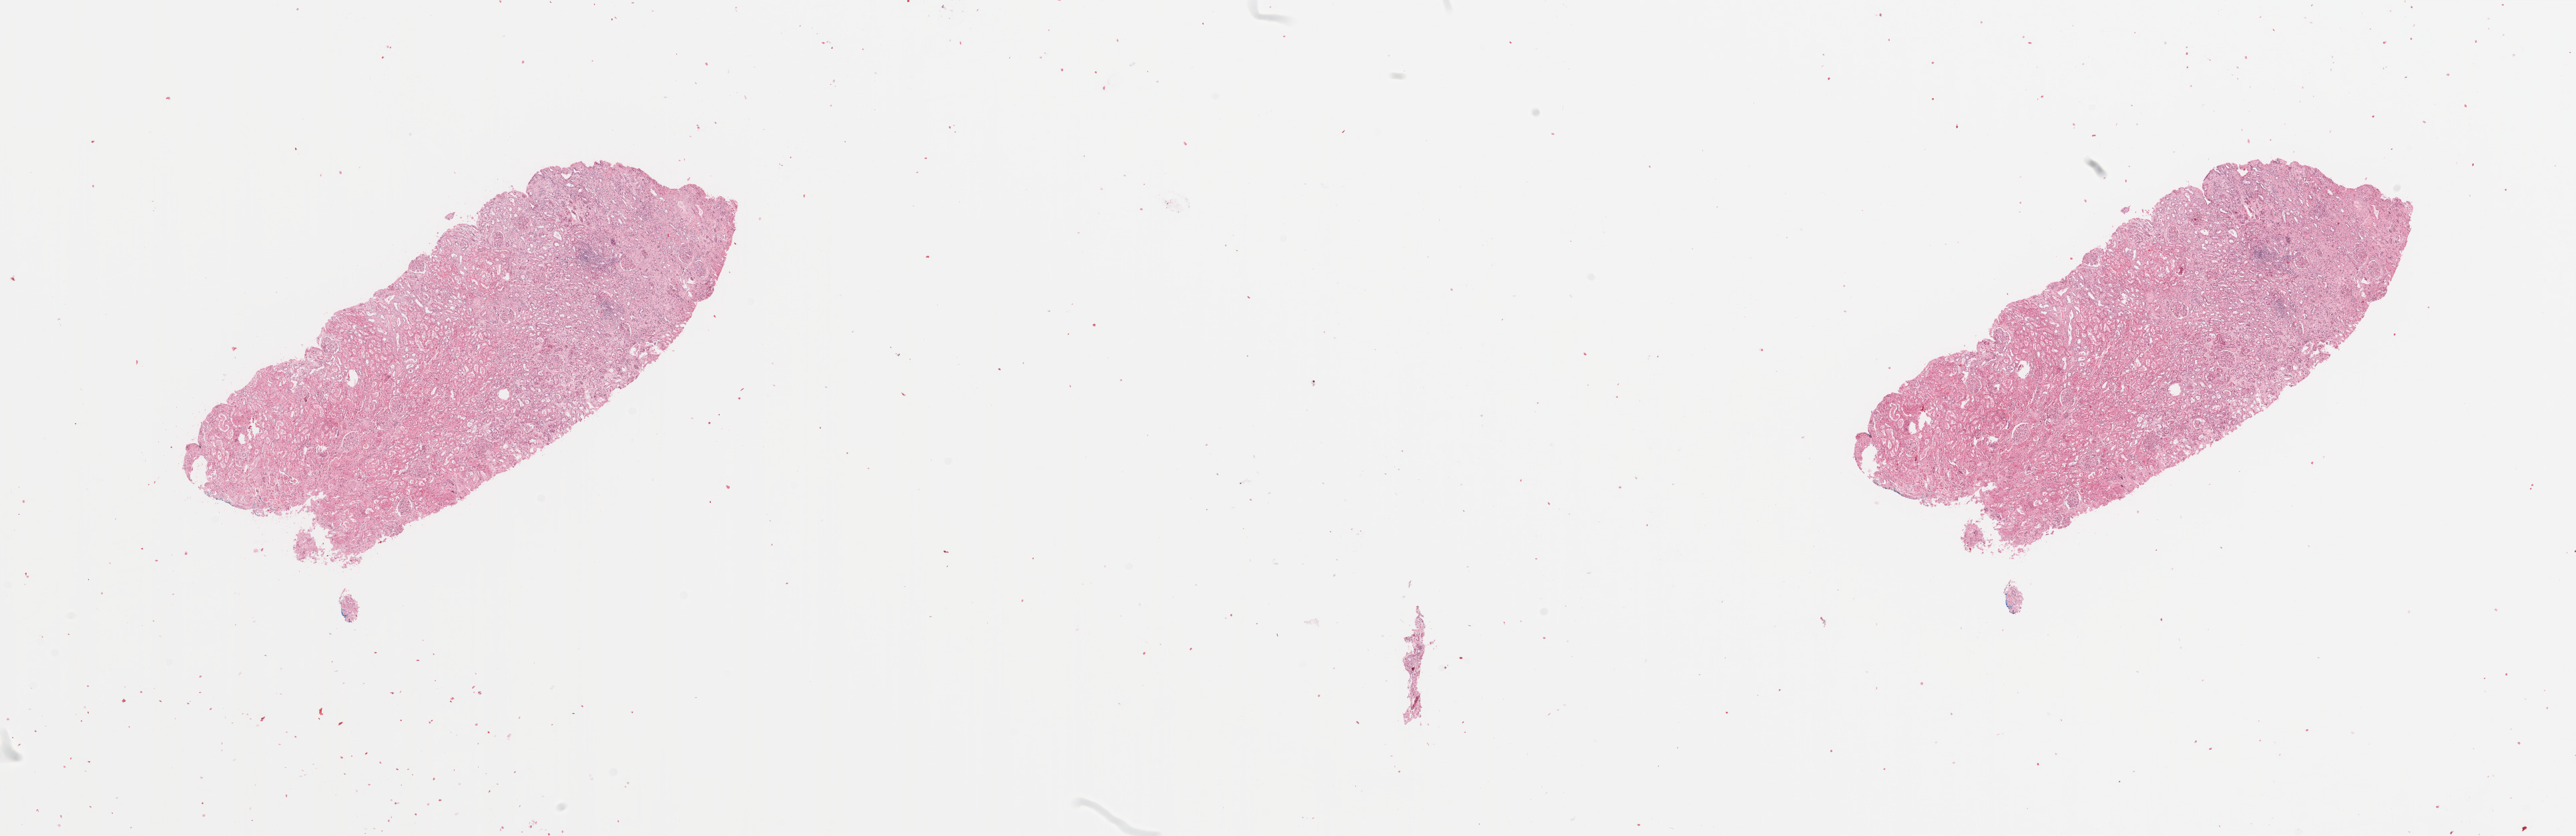
H&E-stained whole-slide image — low-resolution overview of the scanned area, about 30.5 x 9.9 mm (slide scanned at 20x), kidney, normal (non-tumour) tissue. 54-year-old male patient.
This section: normal (non-tumour) tissue from the same patient. Patient diagnosis: Renal cell carcinoma, NOS.